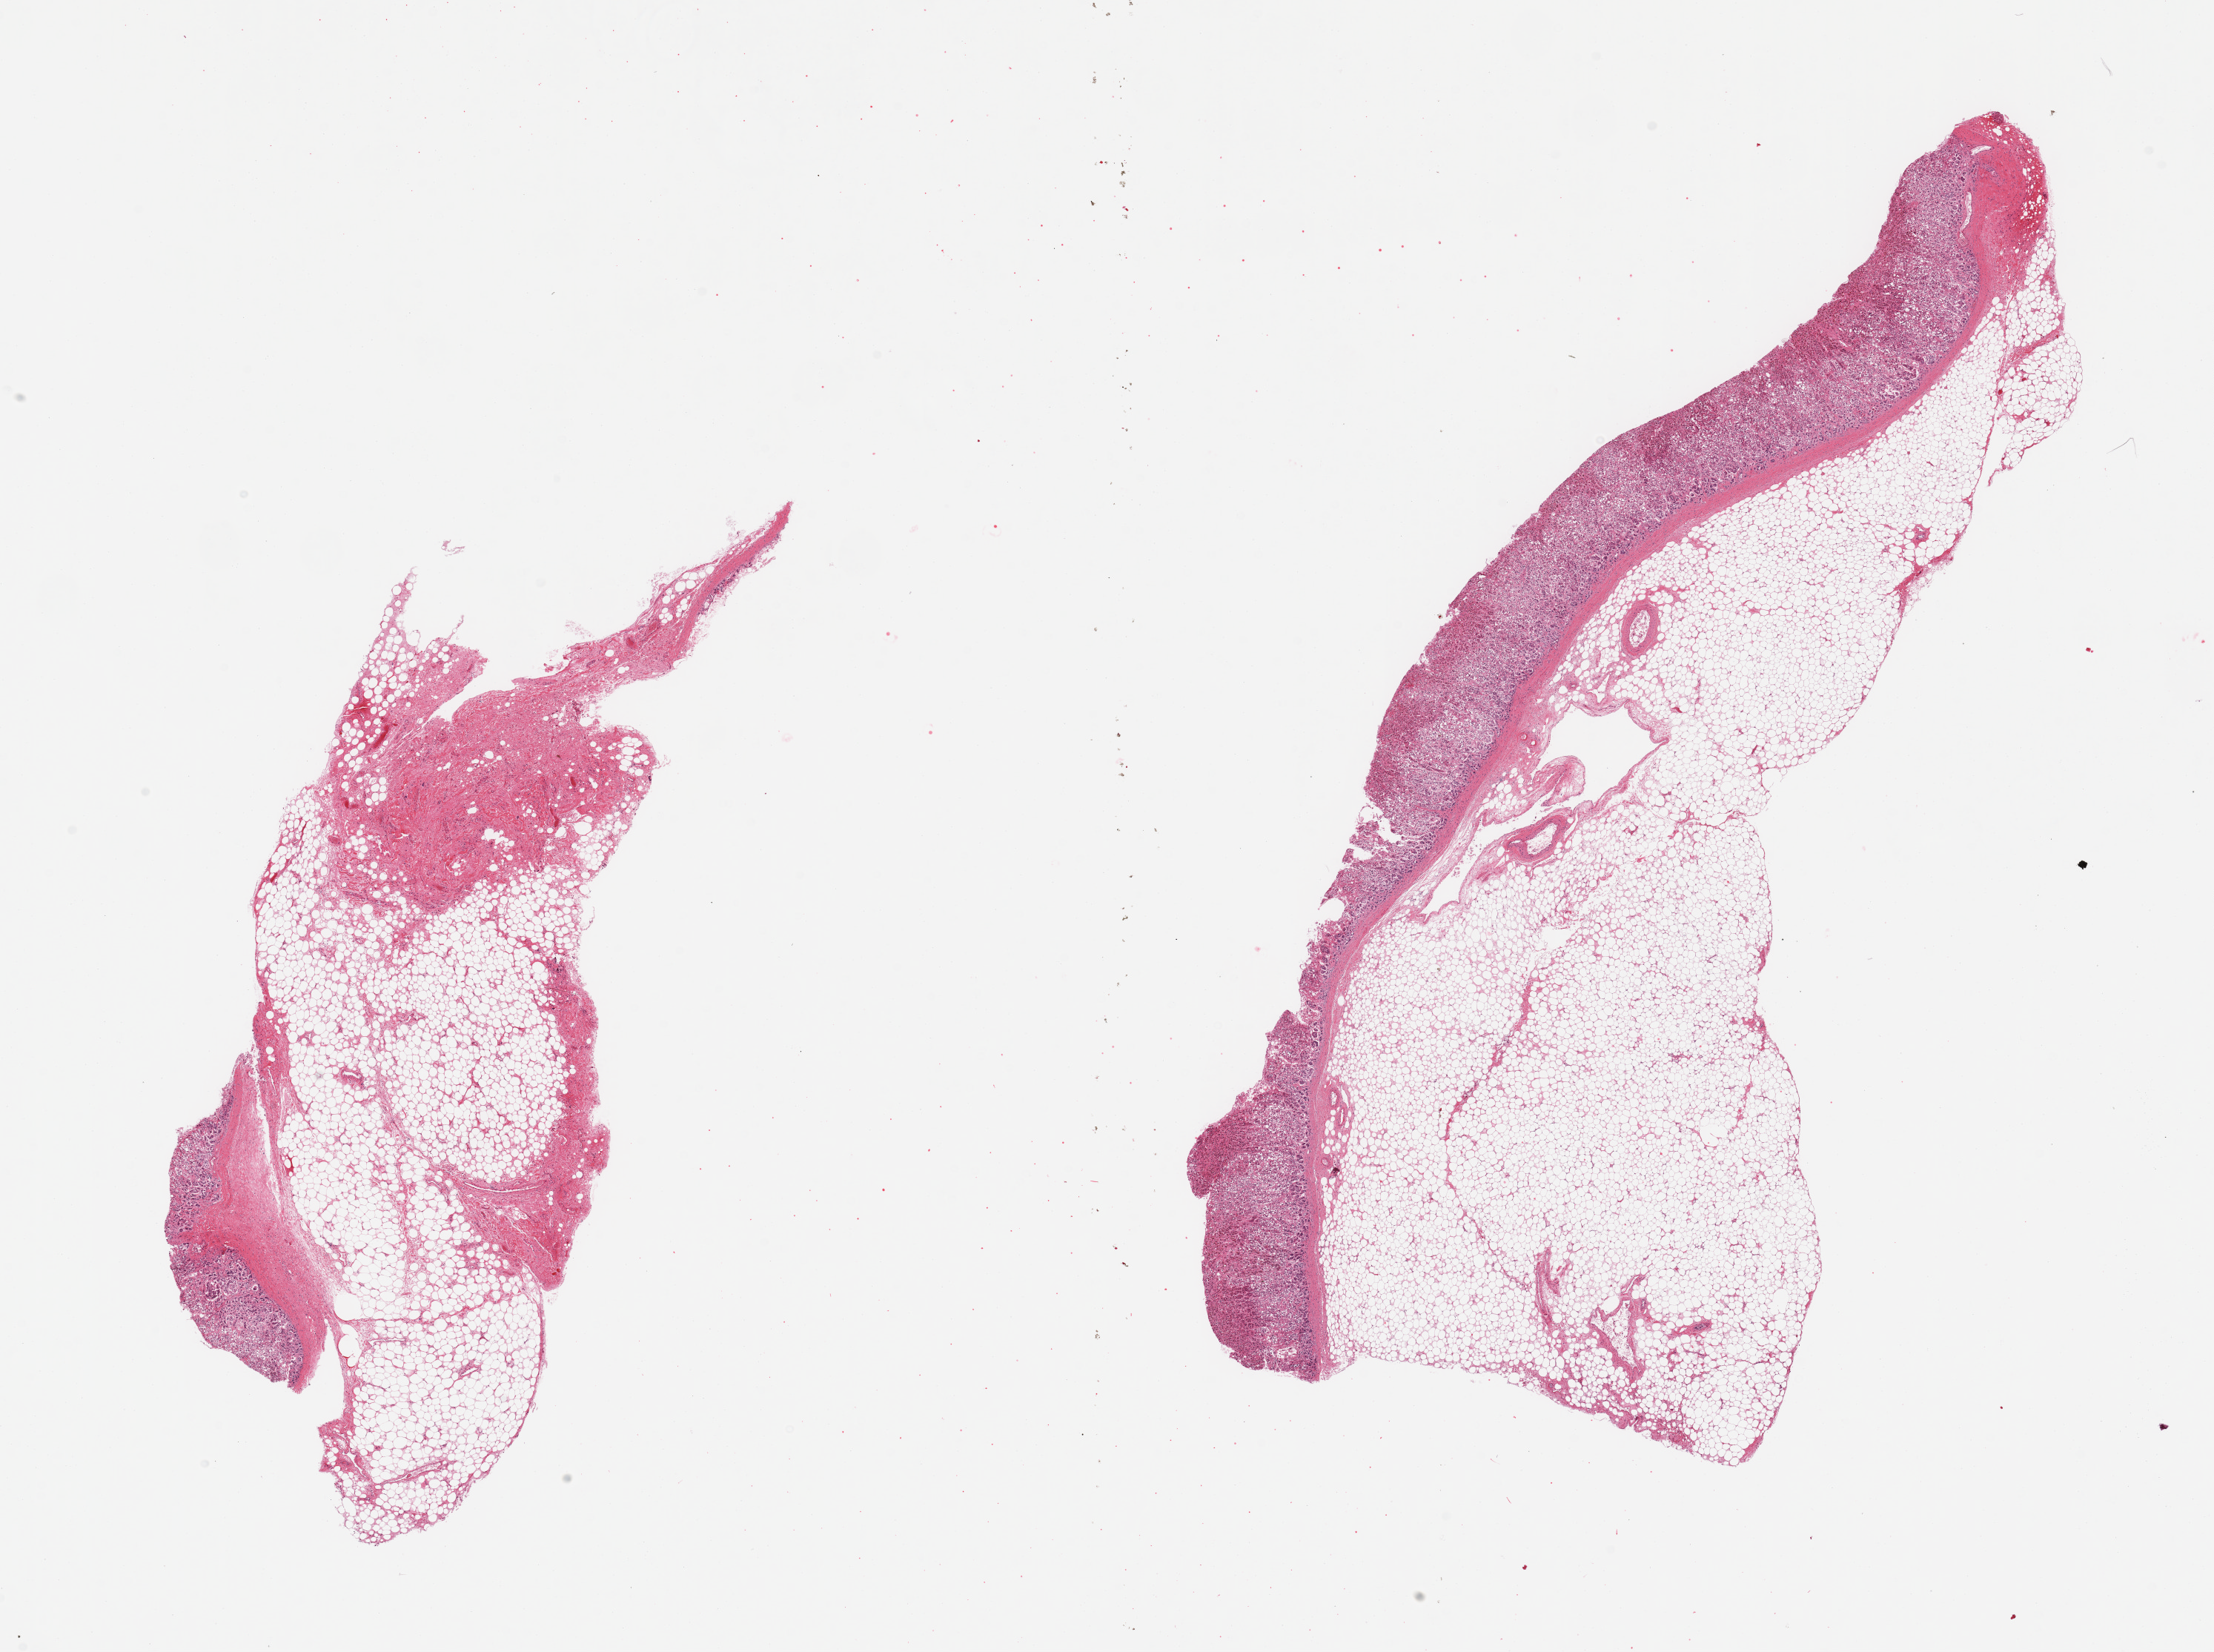
H&E whole-slide image — low-resolution overview of the scanned area, about 23.6 x 17.6 mm; PAXgene-fixed, paraffin-embedded tissue; section of adrenal gland (target tissue); donor tissue sample. Male donor.
Pathologist's review note for this sample: 2 pieces, 1 with 70% fat, other with 80% fibrofatty content.